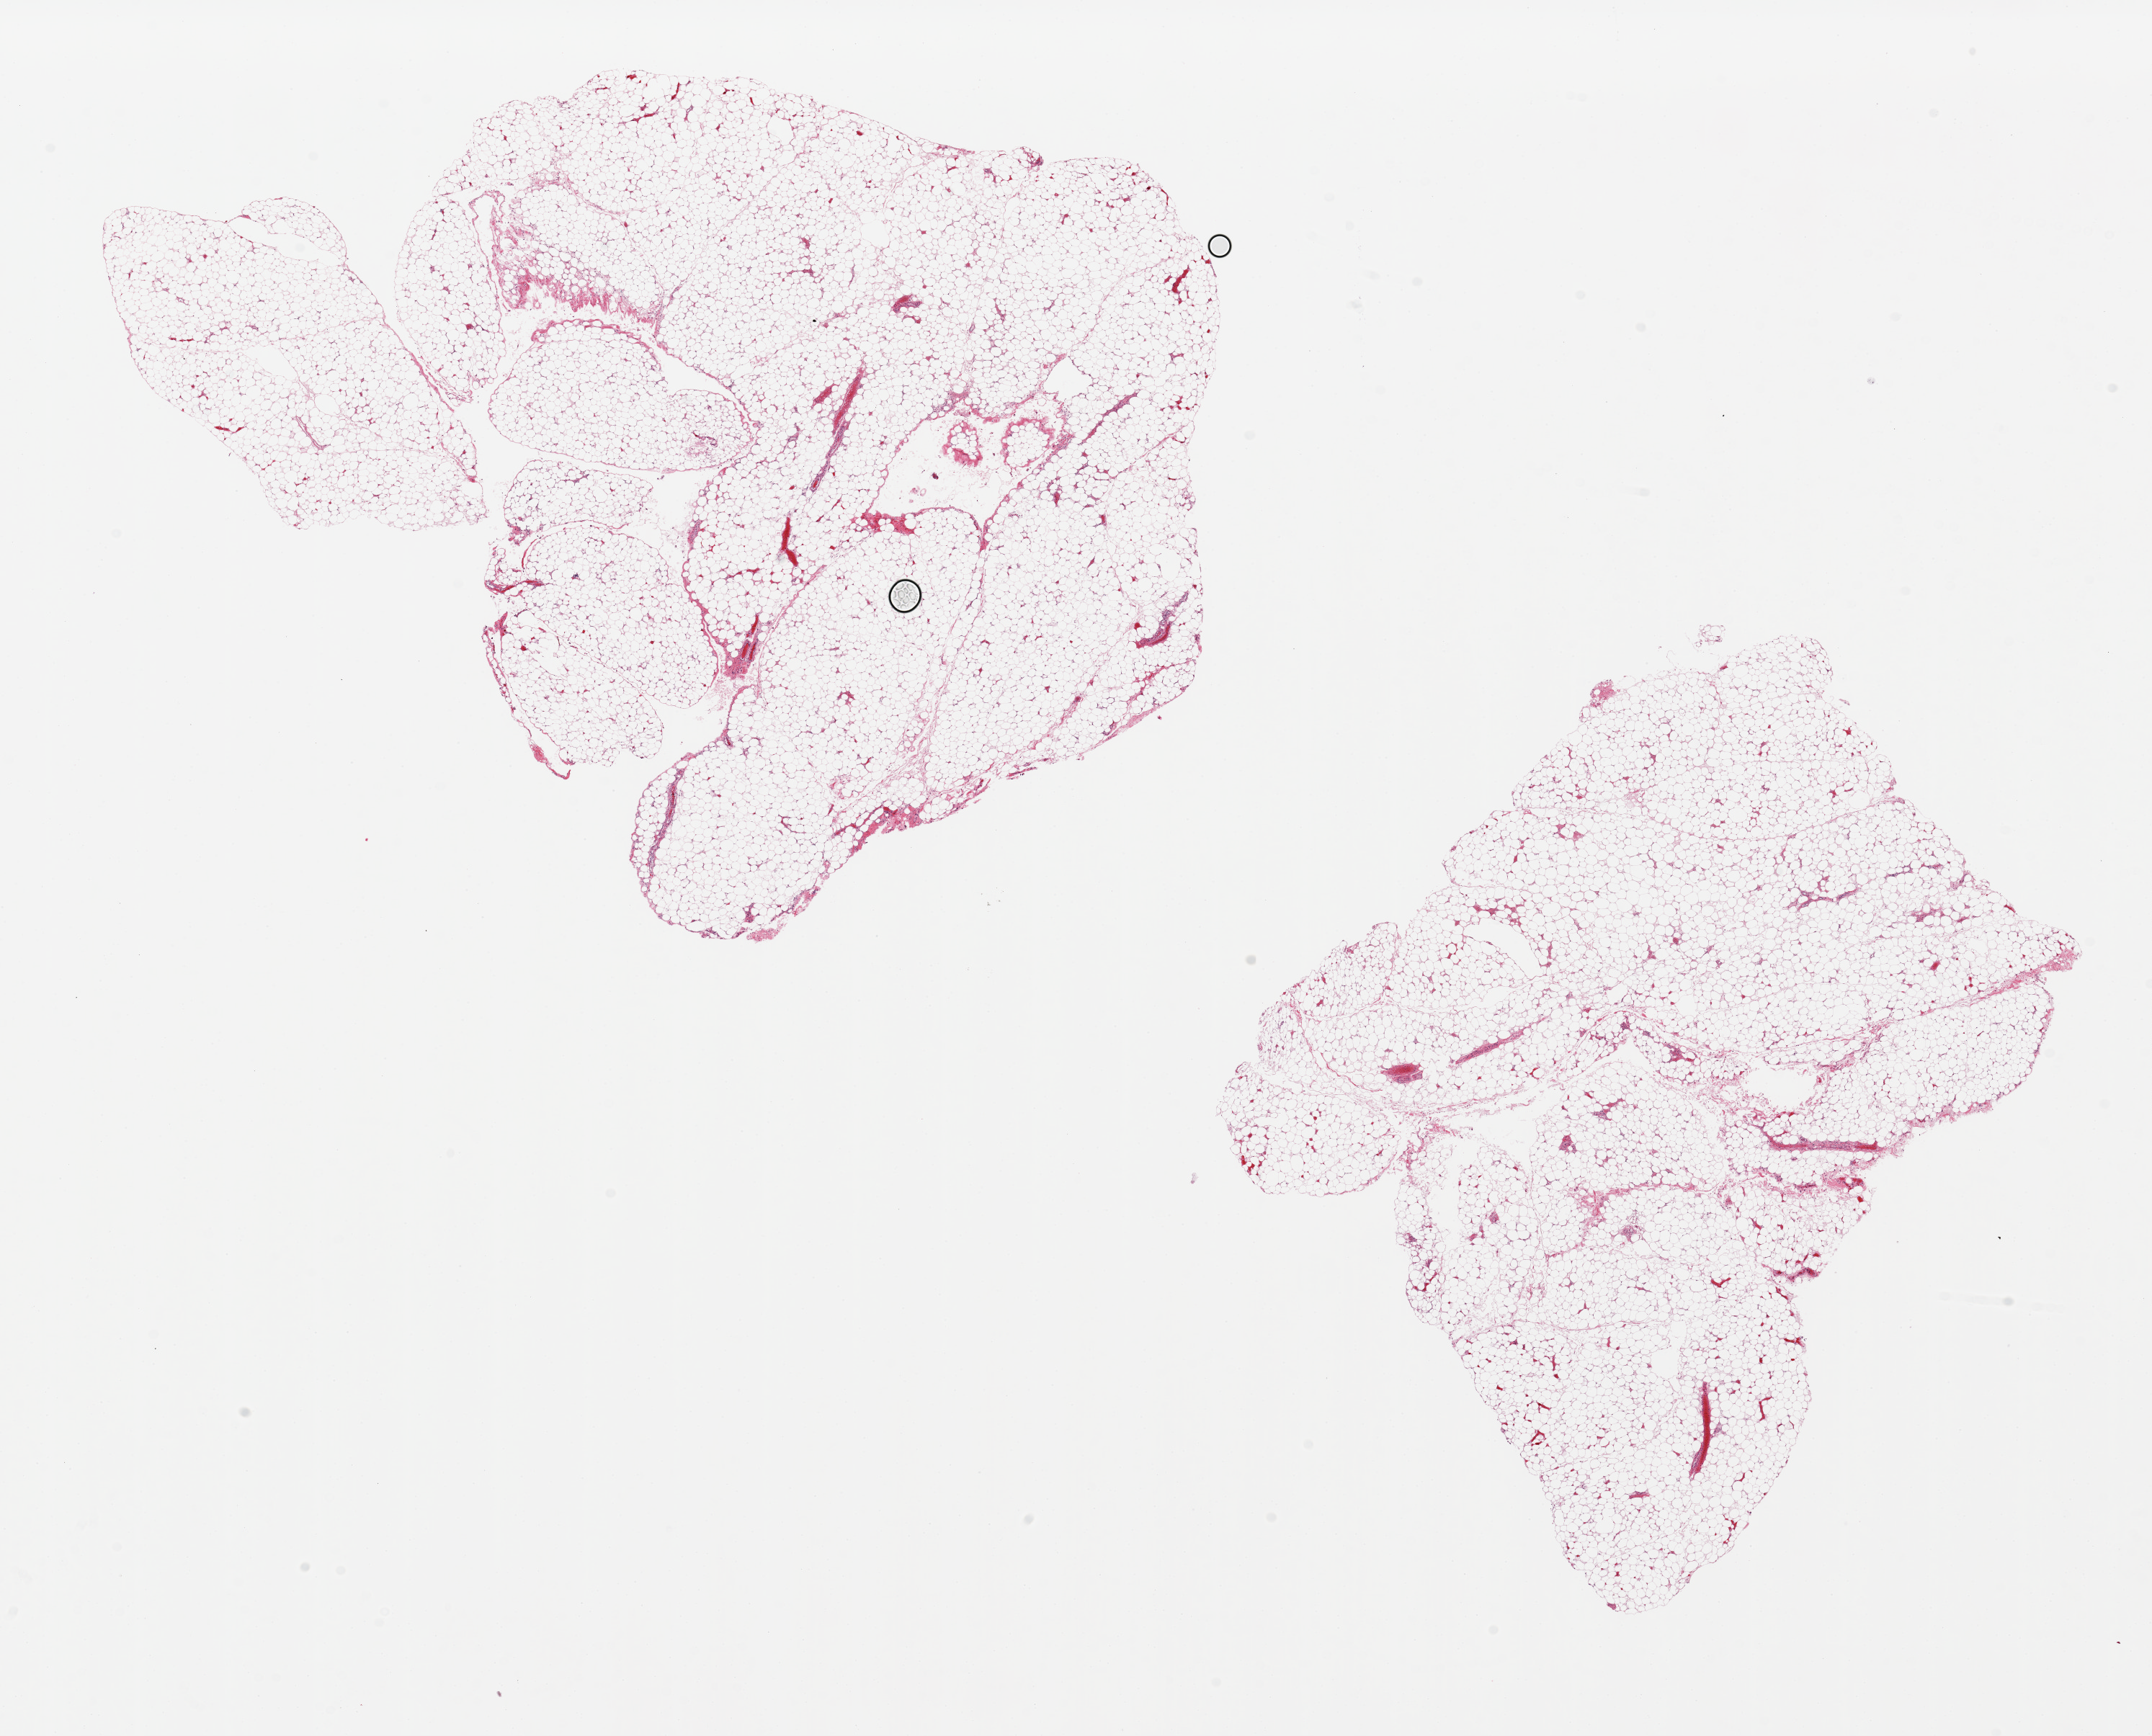
Hematoxylin and eosin (H&E) whole-slide image — whole scanned area (about 23.6 x 19.1 mm, slide scanned at 20x) shown as a low-resolution overview; PAXgene-fixed paraffin-embedded (PFPE) section; target tissue: omentum; donor tissue sample. Donor: male.
Review note (as recorded): 2 pieces ~8x7mm.